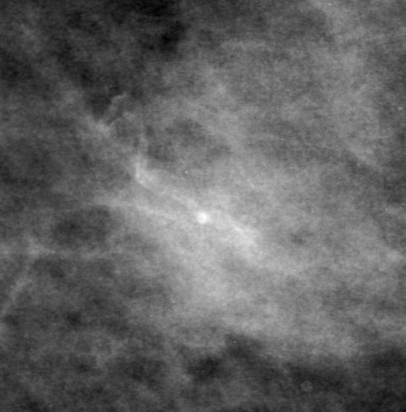
Region of interest cut from a scanned film mammogram (one marked finding), right breast, MLO view.
Finding: mass, shape oval, margins ill defined; BI-RADS assessment category 4; pathology (as recorded): malignant.